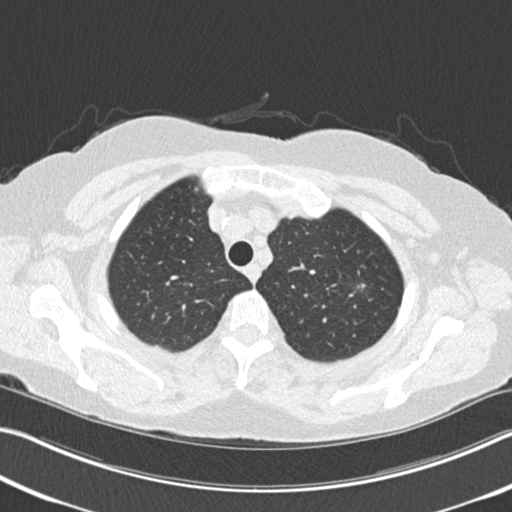
Low-dose screening chest CT, one axial slice. Position 189 of 225 along the scan axis. Reconstruction kernel B30f. 120 kVp. Lung window (W 1500 / L -600 HU). 2 mm slice thickness. 512 × 512 image matrix, field of view 342 × 342 mm.
Structures marked on this image (expert manual segmentation):
- lesion 1 (tumor): bounding box (x1, y1, x2, y2) in pixels: (361, 283, 366, 288)